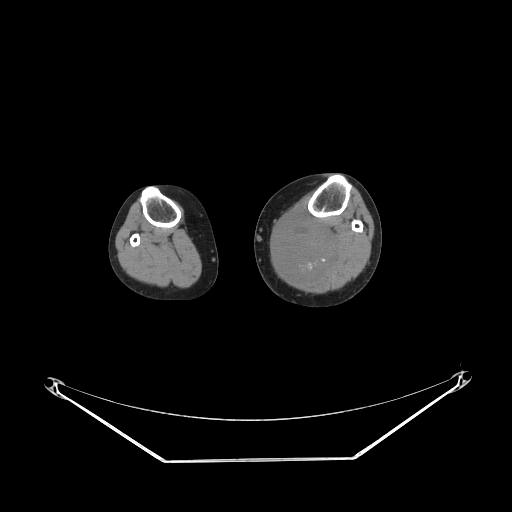
CT of an extremity soft-tissue mass (from a PET/CT study), one axial slice; position 152 of 223 along the scan axis; 140 kVp; soft-tissue window (W 400 / L 40 HU); 3.75 mm slice thickness; 512 × 512 image matrix, field of view 500 × 500 mm. Female patient. From the clinical record (not read from this slice): histological type: extraskeletal high grade osteogenic sarcoma; grade: high; site of the primary tumour: left calf.
Annotated regions visible in this slice (expert contour drawn on MRI and transferred to this co-registered scan by the dataset authors):
- gross tumour volume (mass): bounding box (x1, y1, x2, y2) in pixels: (274, 217, 339, 280)